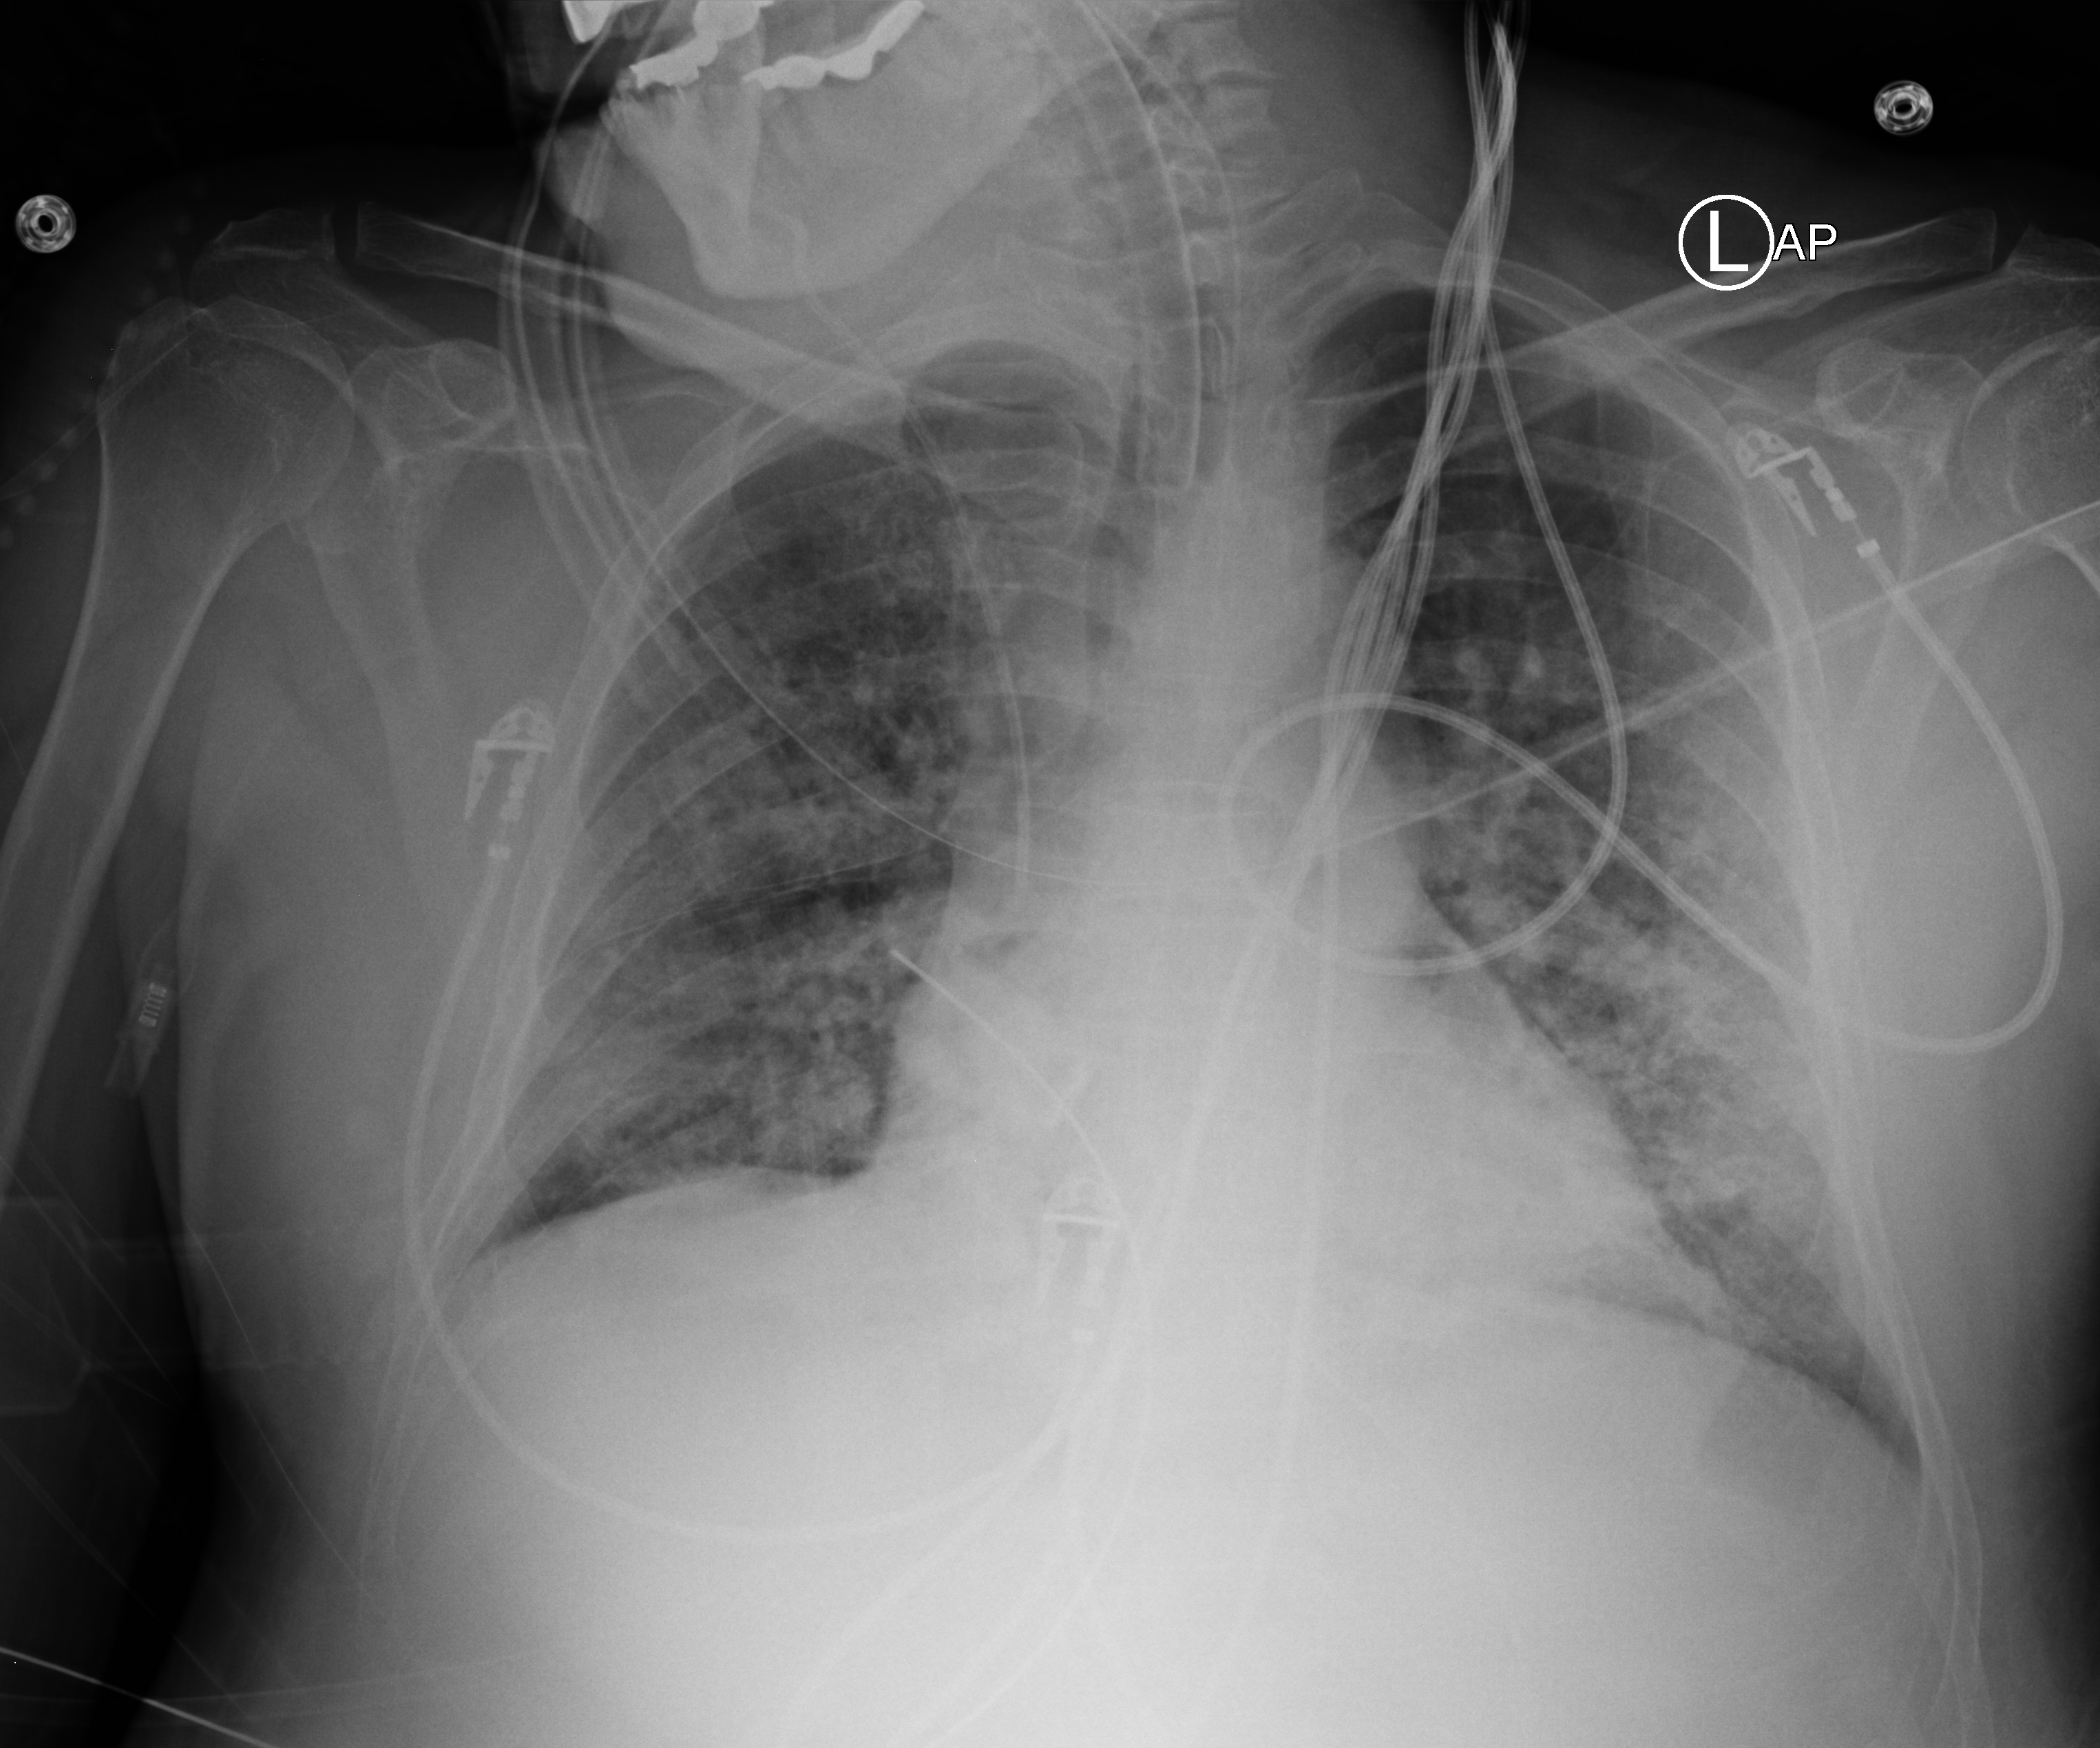
Chest X-ray (portable). Patient hospitalised with COVID-19; male, aged 60–74 years.
Admission-level facts for this patient (not findings on this image; timing relative to this image not recorded): mechanically ventilated during this hospital stay: yes.